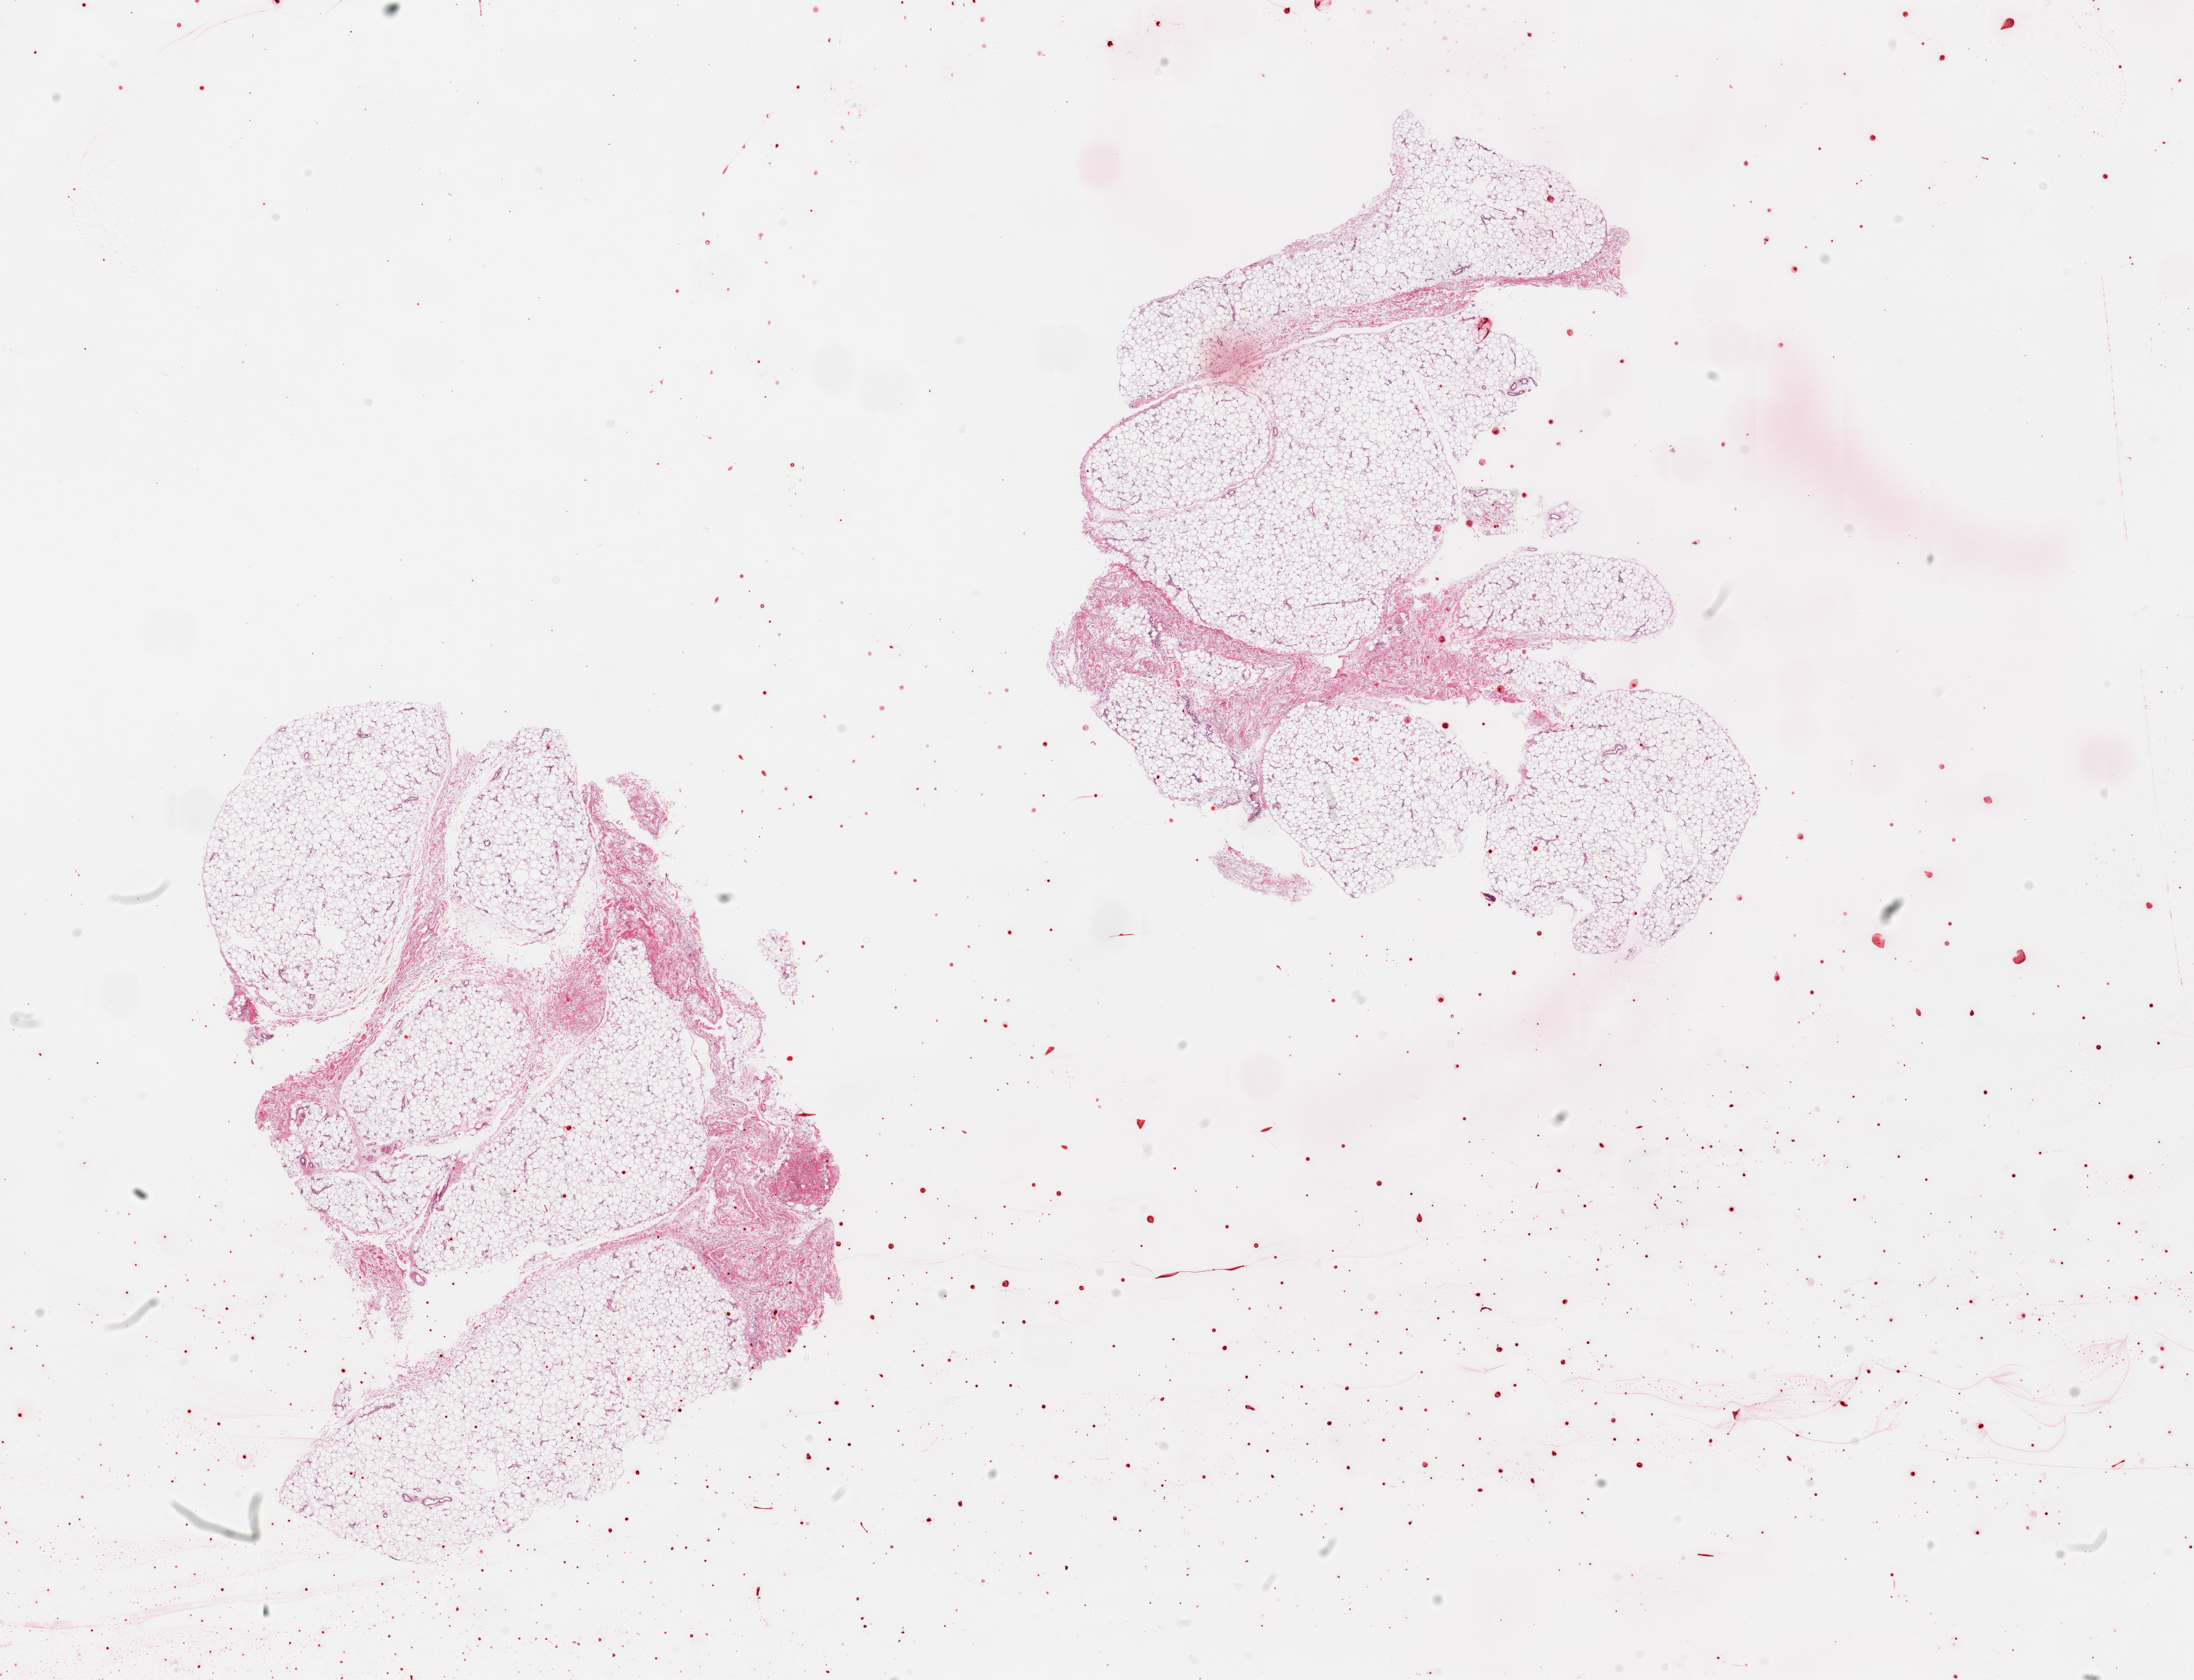
H&E whole-slide image — a low-resolution overview of the entire scanned area, about 24.6 x 18.8 mm; PAXgene-fixed paraffin-embedded (PFPE) section; section of adipose tissue (target tissue); donor tissue sample. Donor sex: male.
Pathologist's review note for this sample: 2 pieces, fascia is 10-15% total.